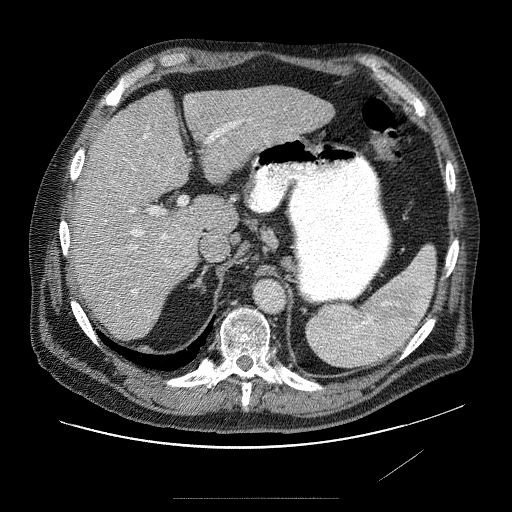
Contrast-enhanced abdominal CT (liver protocol), one axial slice. Position 51 of 89 along the scan axis. Reconstruction kernel STANDARD. 120 kVp. Soft-tissue window (W 400 / L 40 HU). 2.5 mm slice thickness. 512 × 512 image matrix, field of view 420 × 420 mm. Case-level facts recorded for this patient, not image findings: diagnosis: hepatocellular carcinoma (patient treated with transarterial chemoembolisation; whether this scan precedes or follows treatment is not stated here); TNM stage (as recorded): Stage-IVA; Child-Pugh class: A; tumour differentiation: moderately differentiated; tumour nodularity: multinodular.
Outlined on this slice (semi-automatically segmented with operator editing):
- abdominal aorta: bounding box [x1, y1, x2, y2] px = [254, 281, 284, 312]
- liver parenchyma outside the tumour (the mass and vessels are separate outlines, so this box may not span the whole liver): [70, 84, 336, 330]
- mass: [152, 139, 195, 258]
- liver vessels: [103, 117, 276, 298]